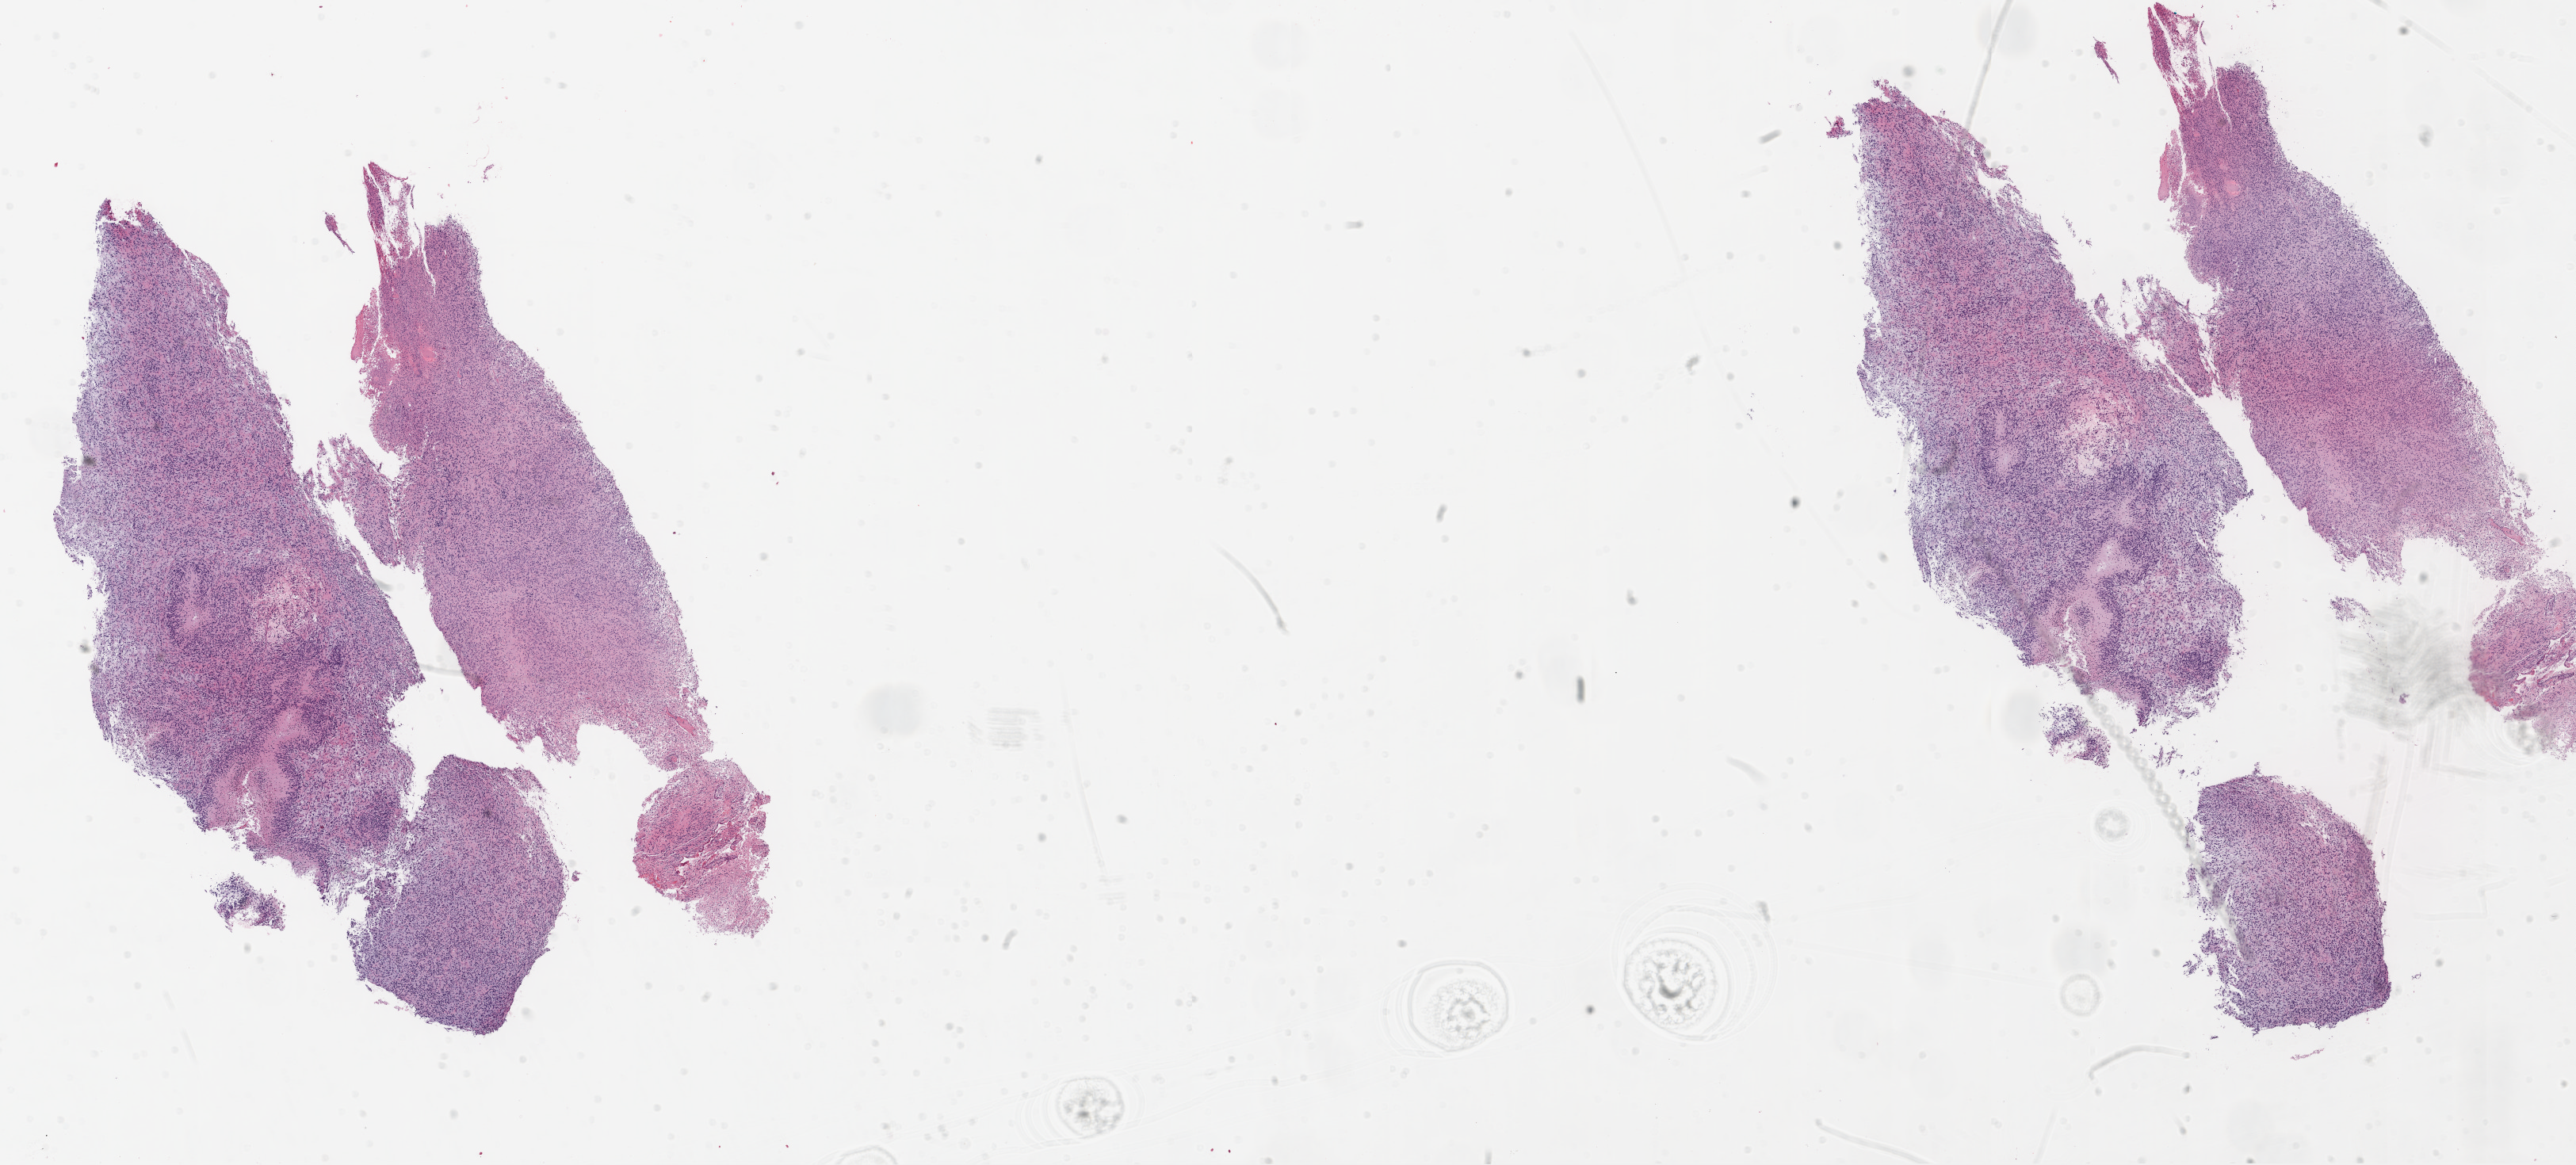
Digitized H&E tissue section (whole slide) — shown as a low-resolution overview of the whole scanned area (about 26.1 x 11.8 mm, from a 20x scan); formalin-fixed paraffin-embedded (FFPE) diagnostic section; primary tumour sample from the brain. Patient: female, age at initial diagnosis 63 years.
- pathologic diagnosis: Glioblastoma